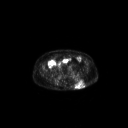
FDG PET of an extremity soft-tissue mass (from a PET/CT study), one axial slice; slice 79 of 267 in the series (ordered by position); 3.27 mm slice thickness; 128 × 128 image matrix, field of view 700 × 700 mm. Male patient, age 69 years. Case-level facts recorded for this patient, not image findings: histological type: leiomyosarcoma; grade: intermediate; site of the primary tumour: left pelvis.
Annotated regions visible in this slice (expert contour drawn on MRI and transferred to this co-registered scan by the dataset authors):
- gross tumour volume (mass): bounding box <74,79,85,89> (left, top, right, bottom; pixels)